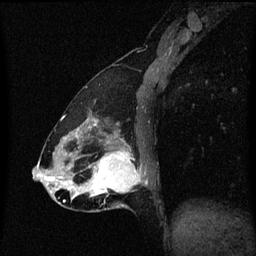
Breast MRI (dynamic contrast-enhanced), one sagittal slice; slice 24 of 60 in the series (ordered by position); dynamic contrast-enhanced series, image 2 of 3 at this slice position (ordered by acquisition); 1.5 T; TE 4.2 ms, TR 8.4 ms; 2 mm slice thickness; 256 × 256 image matrix, field of view 200 × 200 mm. Female patient, age 47 years.
Annotated regions visible in this slice (semi-automatically segmented with operator editing):
- analysis volume of interest (the breast-tissue region the enhancement analysis was run in; not a lesion): bounding box (x1, y1, x2, y2) in pixels: (81, 138, 147, 213)
- tumour enhancement mask (voxels above the 70 % enhancement threshold inside the analysis volume of interest): (85, 142, 141, 197)